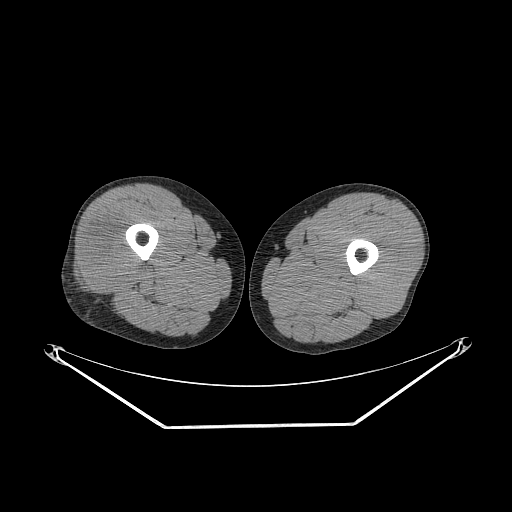
CT of an extremity soft-tissue mass (from a PET/CT study), one axial slice; slice 237 of 267 in the series (ordered by position); 140 kVp; soft-tissue window (W 400 / L 40 HU); 3.75 mm slice thickness; 512 × 512 image matrix, field of view 500 × 500 mm. Male patient. From the clinical record (not read from this slice): histological type: poorly differentiated synovial sarcoma; grade: high; site of the primary tumour: right buttock.
Structures marked on this image (expert contour drawn on MRI and transferred to this co-registered scan by the dataset authors):
- gross tumour volume including surrounding oedema: box from (x=80, y=219) to (x=134, y=289) px
- gross tumour volume (mass): (x=84, y=228)–(x=134, y=289)